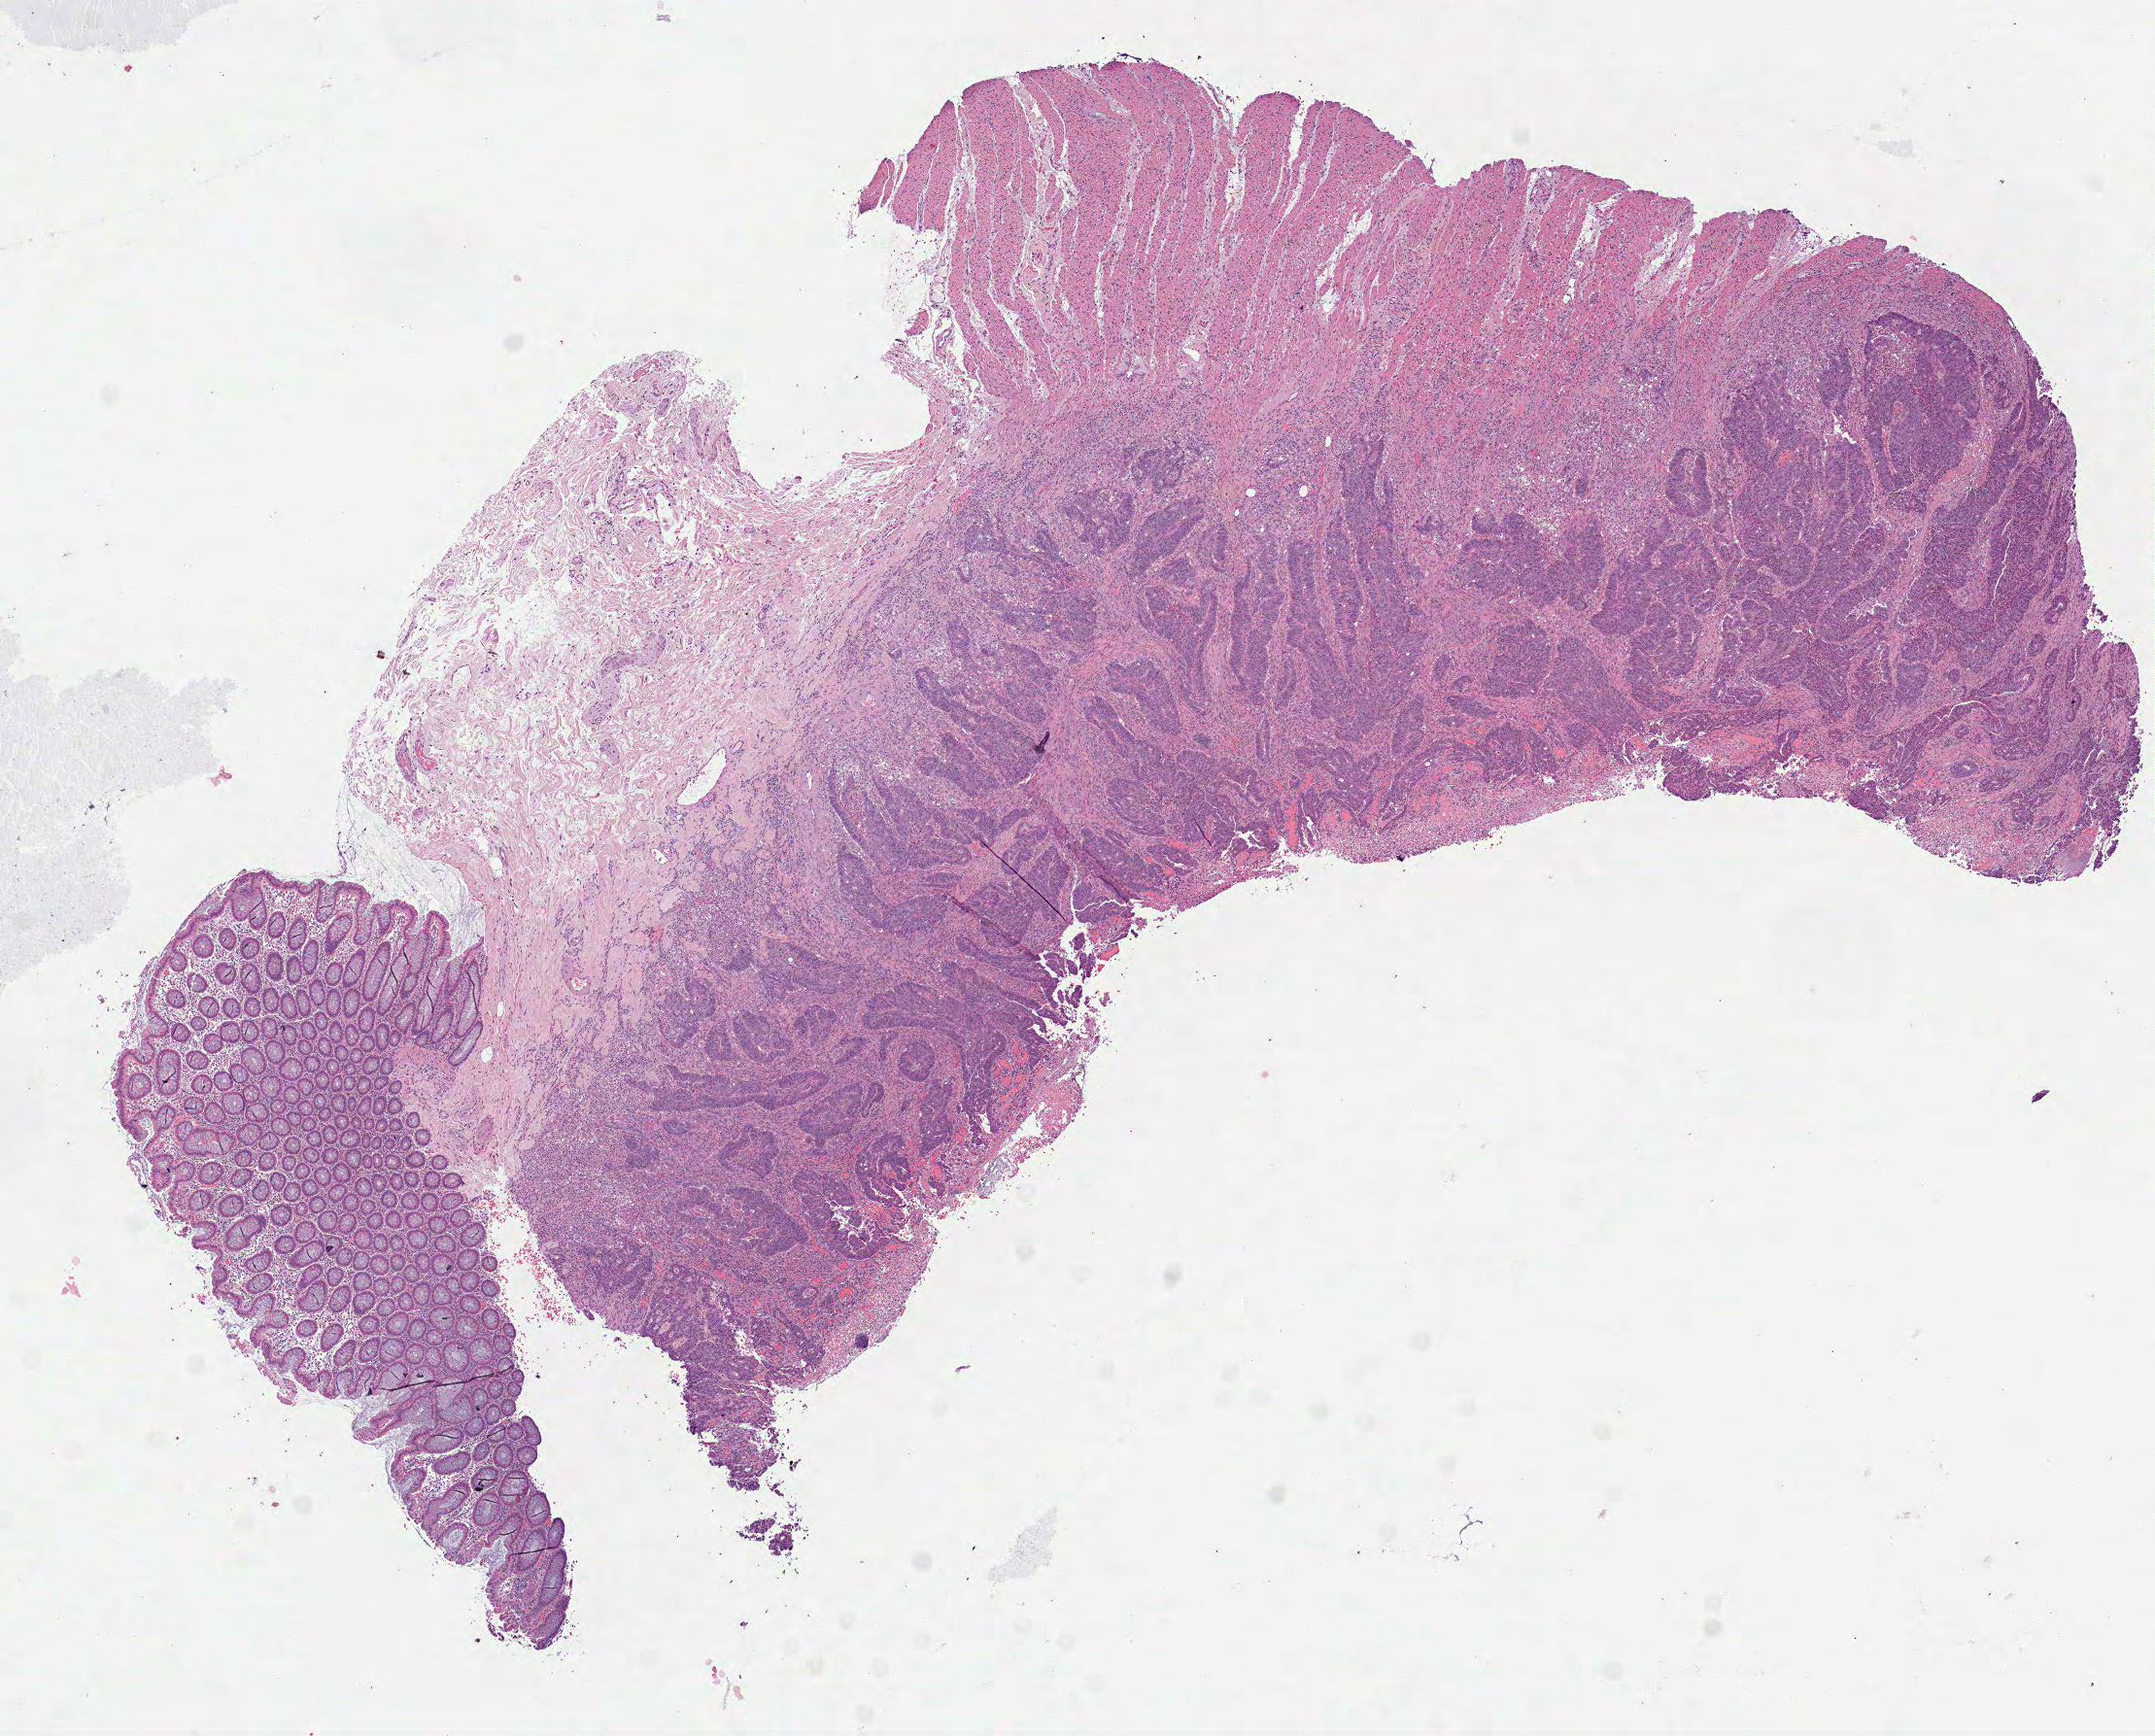
Digitized H&E tissue section (whole slide) — low-resolution overview of the scanned area, about 8.9 x 7.2 mm (slide scanned at 40x). Formalin-fixed paraffin-embedded (FFPE) diagnostic section. Colon, primary tumour sample. Female patient; age at initial diagnosis 81 years.
Pathologic diagnosis: Adenocarcinoma, NOS (splenic flexure of colon). AJCC pathologic stage: I (7th edition). TNM: T2 N0 M0.